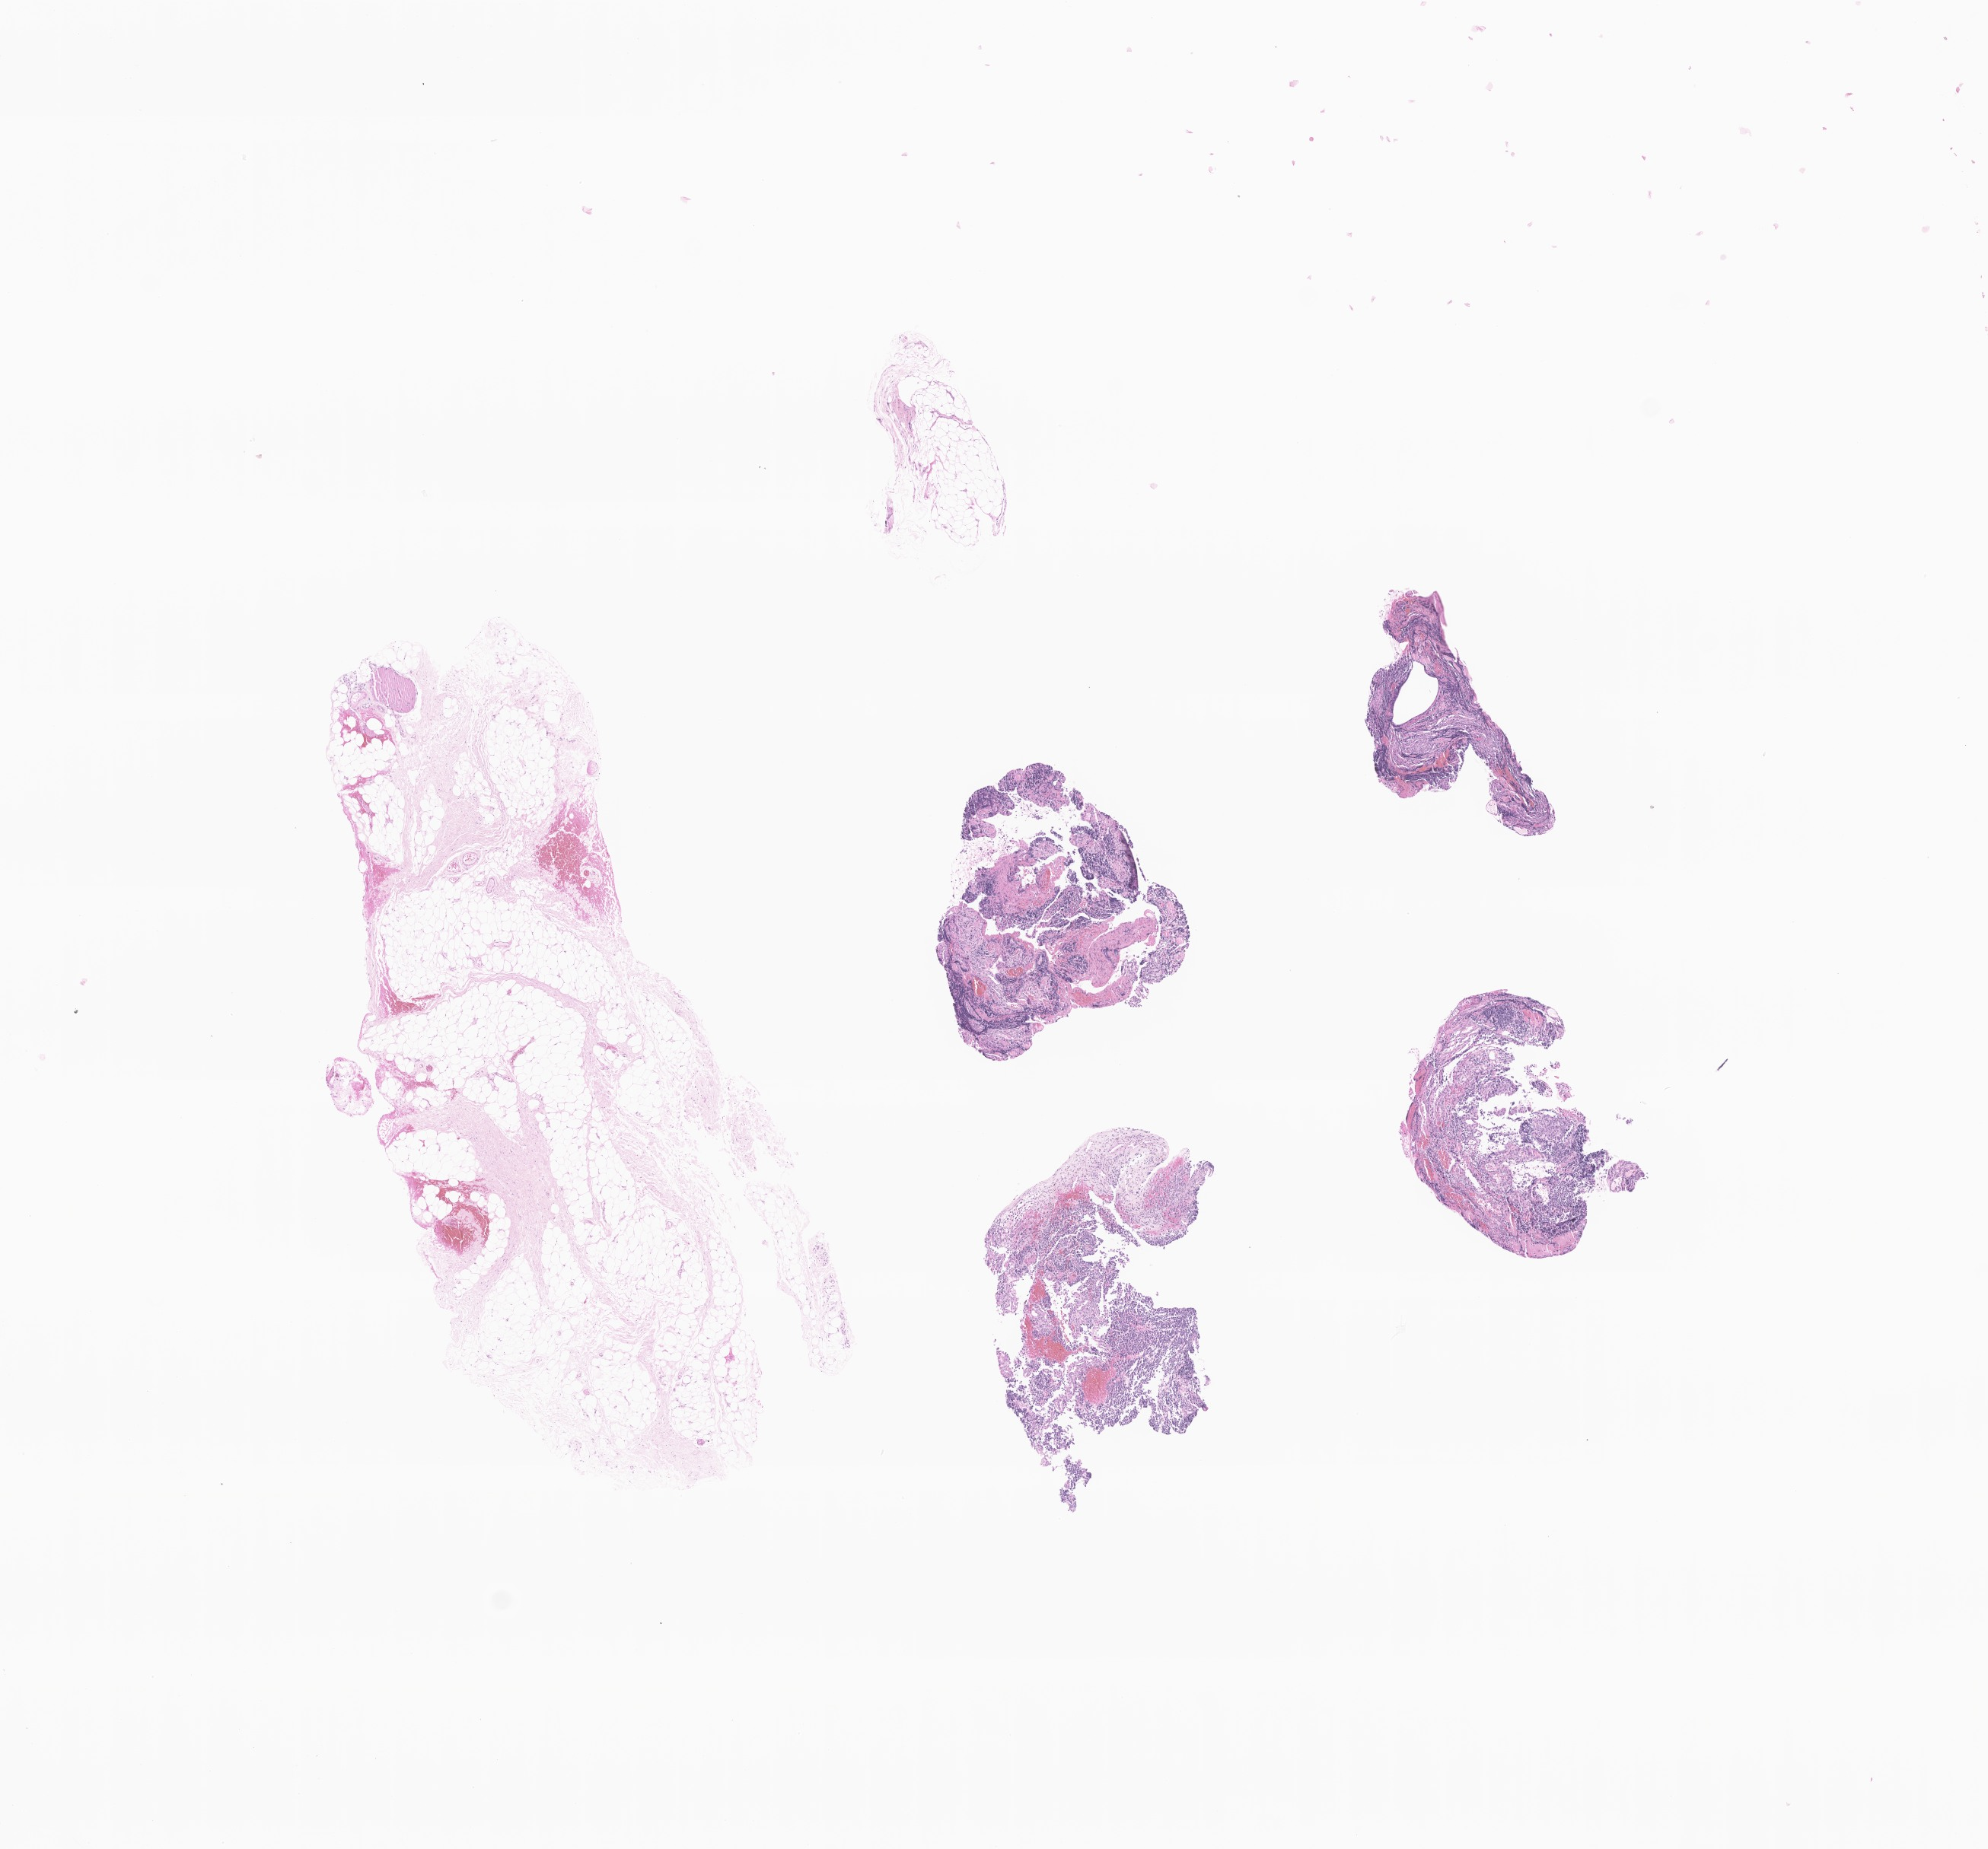
Hematoxylin and eosin (H&E) whole-slide image of tumor tissue from the orbit — shown as a low-resolution overview of the whole scanned area (about 11.0 x 10.2 mm). FFPE section. Patient: male, age 38 months (3 years 2 months).
* recorded diagnosis: Rhabdomyosarcoma, NOS